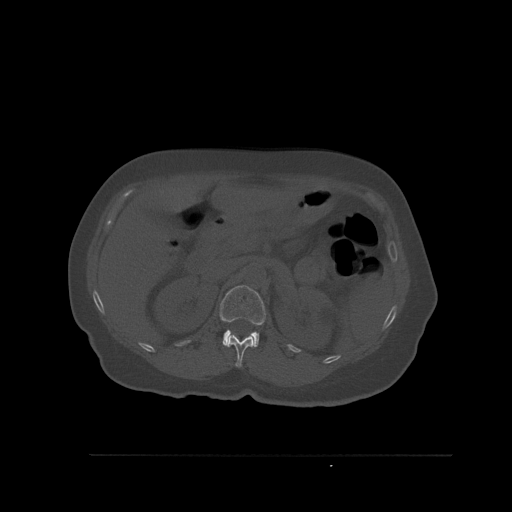
CT including the spine, one axial slice; position 275 of 527 along the scan axis; bone window (W 1800 / L 400 HU); 512 × 512 image matrix, field of view 470 × 470 mm. Female patient, age 73 years. Case-level facts recorded for this patient, not image findings: primary cancer: breast; vertebrae with lytic lesions (as recorded): L2.
Structures marked on this image (semi-automatically segmented with operator editing):
- L1 vertebra: bounding box <219,285,266,348> (left, top, right, bottom; pixels)
- T12 vertebra: <228,333,254,368>